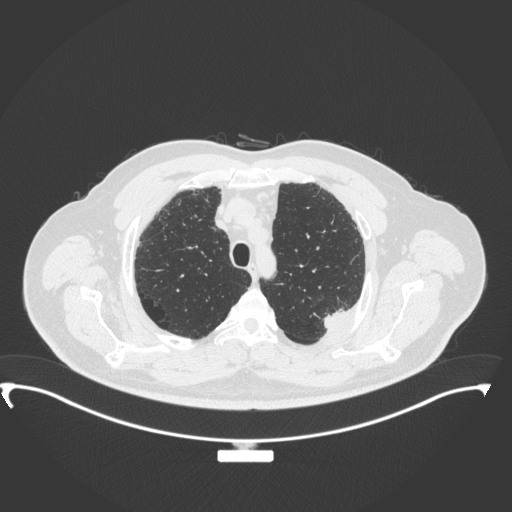
Chest CT, one axial slice. Position 290 of 350 along the scan axis. 120 kVp. Lung window (W 1500 / L -600 HU). 1 mm slice thickness. 512 × 512 image matrix, field of view 459 × 459 mm. Patient: male, 64 years. From the clinical record (not read from this slice): clinical TNM (as recorded): T1c N1 M1.
Annotated regions visible in this slice (rectangle marked by the reading radiologist):
- lung tumour (recorded histology: adenocarcinoma): box from (x=317, y=303) to (x=351, y=333) px